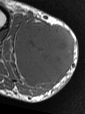
MRI of an extremity soft-tissue mass, one axial slice. Position 25 of 47 along the scan axis. MR volume resampled by the dataset authors to the PET/CT grid (not the native acquisition matrix). 3.27 mm slice thickness. 85 × 114 image matrix, field of view 83 × 111 mm. Male patient. From the clinical record (not read from this slice): histological type: pleiomorphic liposarcoma; grade: high; site of the primary tumour: right calf.
Structures marked on this image (expert contour drawn on MRI and transferred to this co-registered scan by the dataset authors):
- gross tumour volume including surrounding oedema: bounding box [x1, y1, x2, y2] px = [15, 21, 73, 86]
- gross tumour volume (mass): [15, 23, 73, 83]